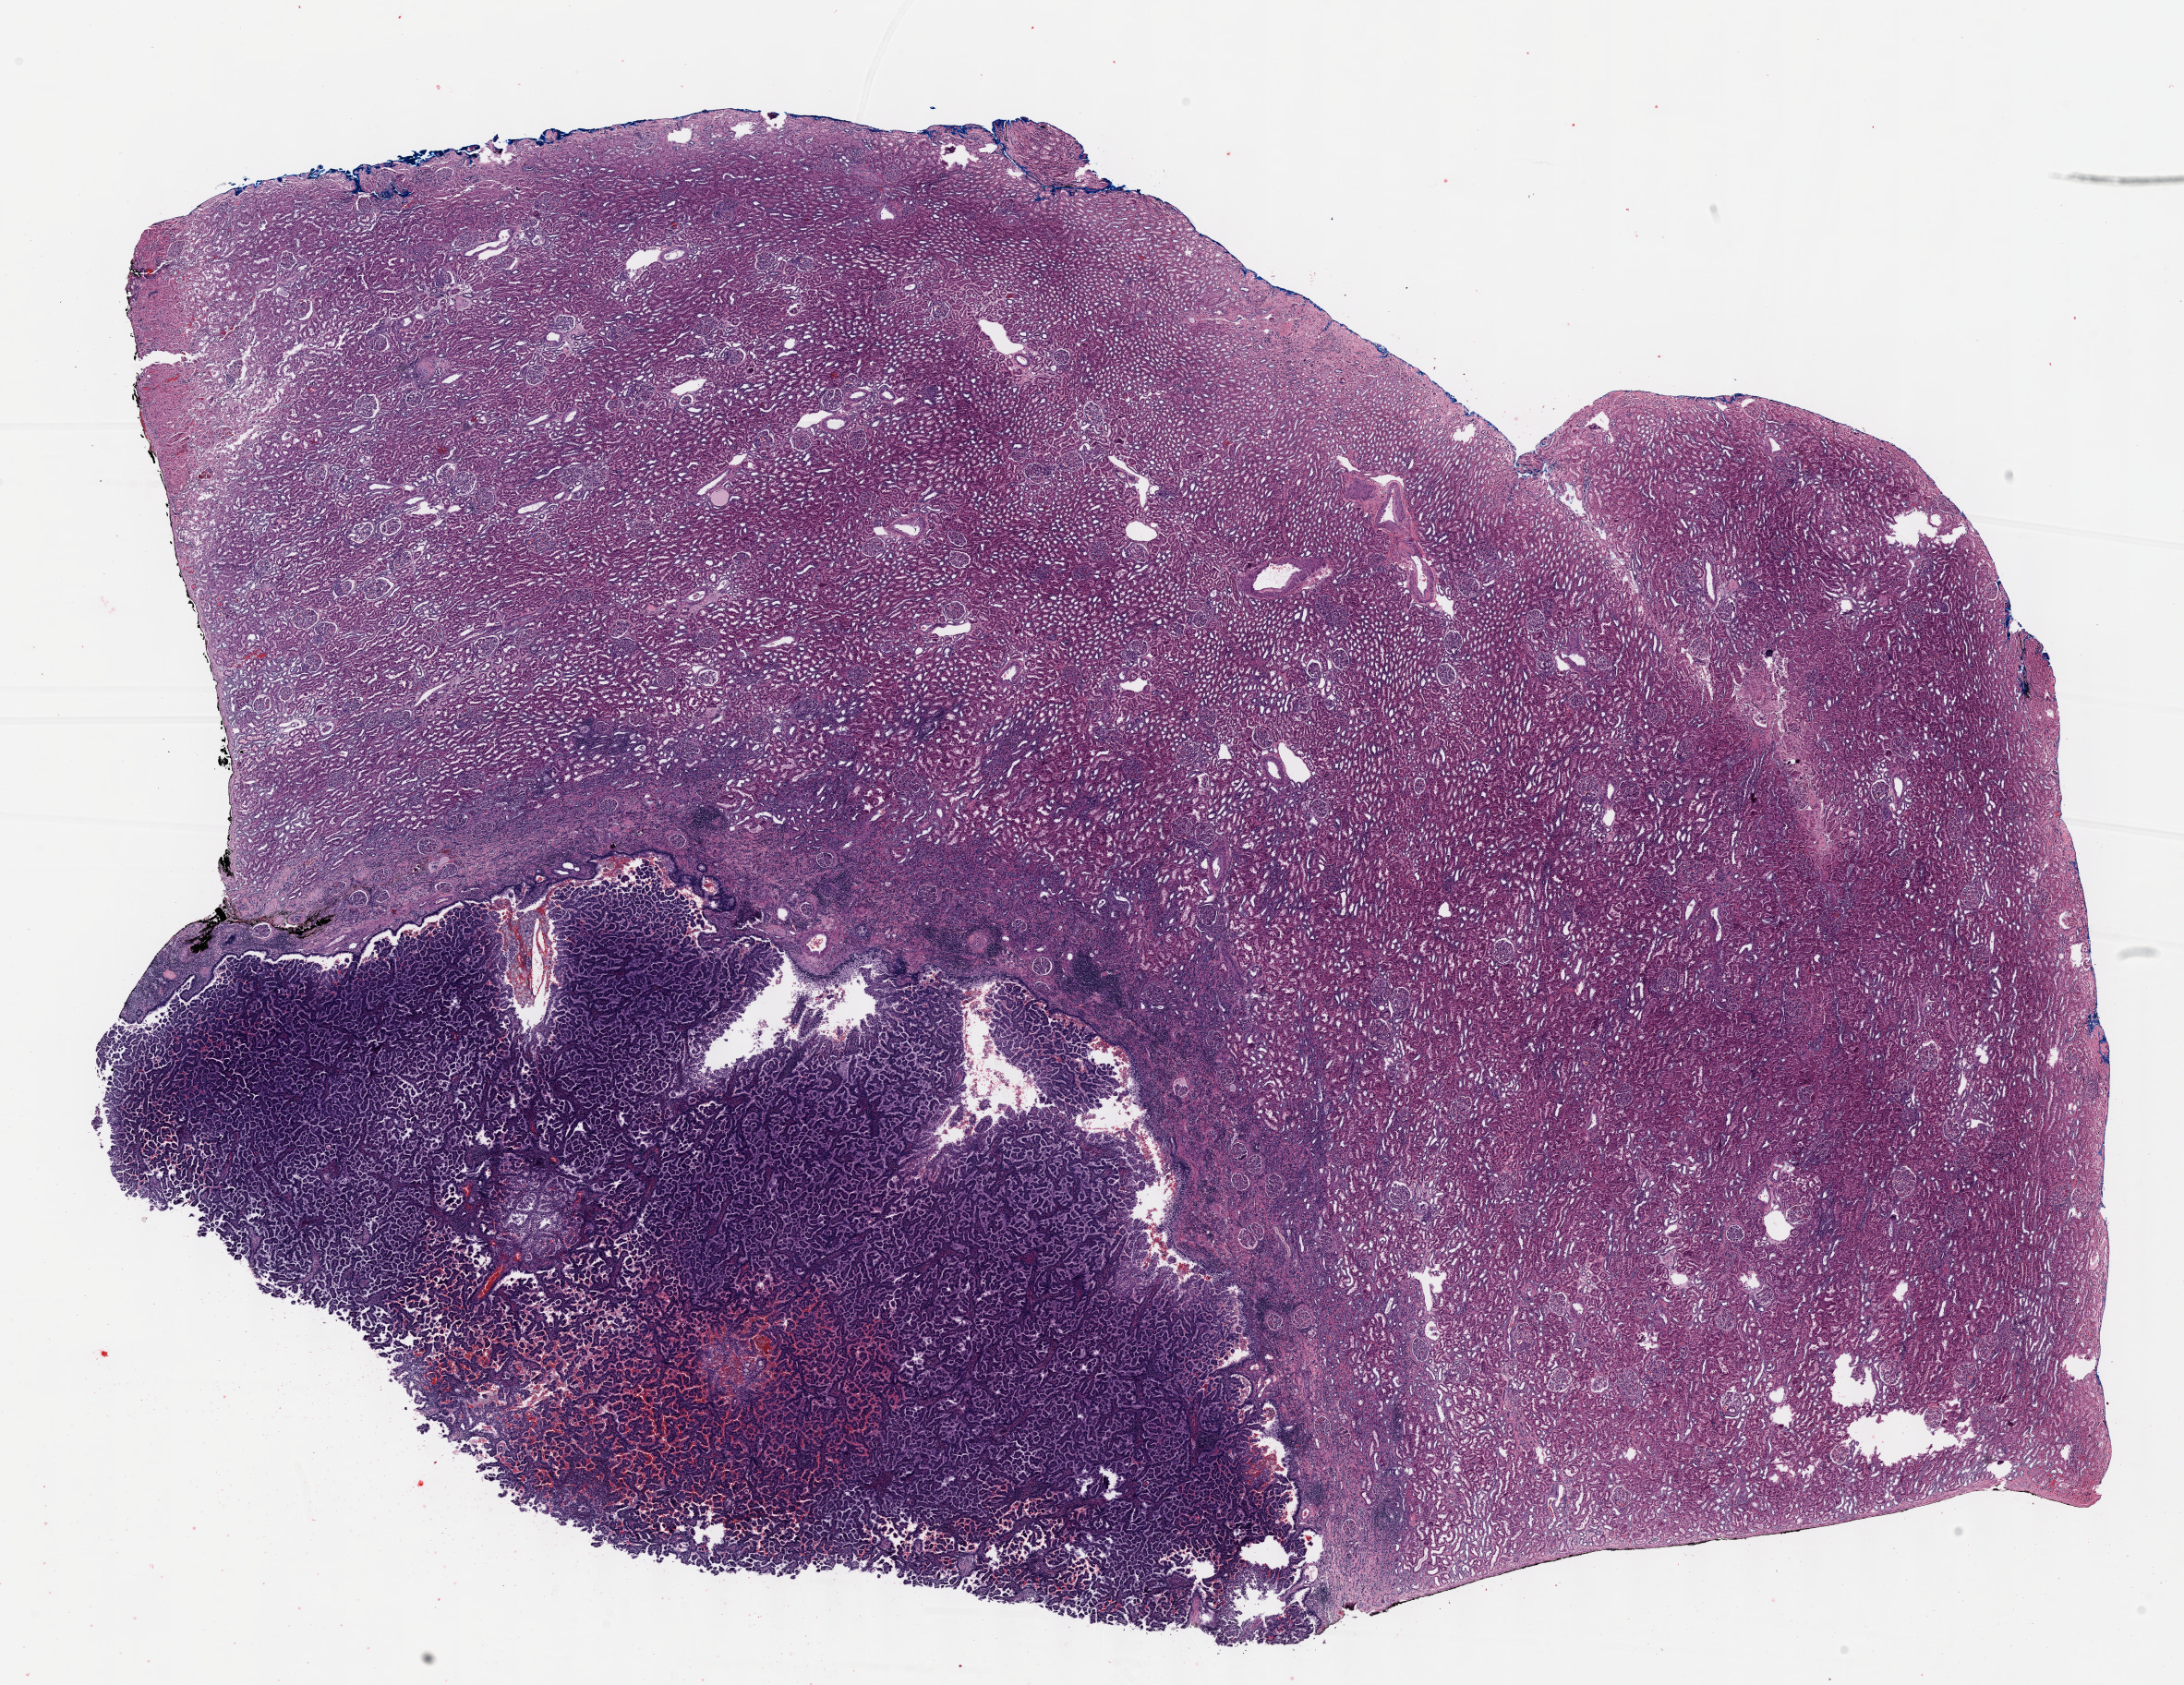
Digitized H&E-stained tissue section (whole slide) — whole scanned area (about 19.1 x 14.7 mm, slide scanned at 40x) shown as a low-resolution overview, FFPE section, sample: primary tumour, kidney. Male patient; age at initial diagnosis 40 years.
• pathologic diagnosis: Papillary adenocarcinoma, NOS
• AJCC pathologic stage: I (7th edition)